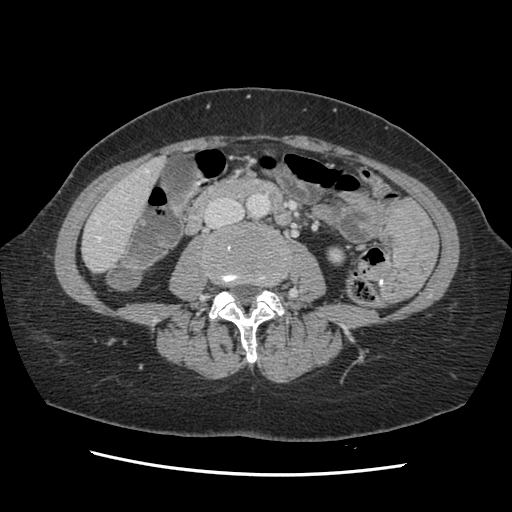
Contrast-enhanced abdominal CT, one axial slice; slice 33 of 141 in the series (ordered by position); 120 kVp; soft-tissue window (W 400 / L 40 HU); 2.5 mm slice thickness; 512 × 512 image matrix, field of view 330 × 330 mm. Female patient, age 61 years. Case-level facts recorded for this patient, not image findings: diagnosis: colorectal cancer liver metastases, imaged before liver resection; multiple liver metastases: no; largest metastasis: 2.4 cm; disease in both lobes: no.
Annotated regions visible in this slice (outlined manually by an expert reader):
- hepatic veins: bounding box <95,169,149,240> (left, top, right, bottom; pixels)
- liver: <84,160,162,272>
- planned liver remnant (the part of the liver to remain after resection): <84,161,162,272>